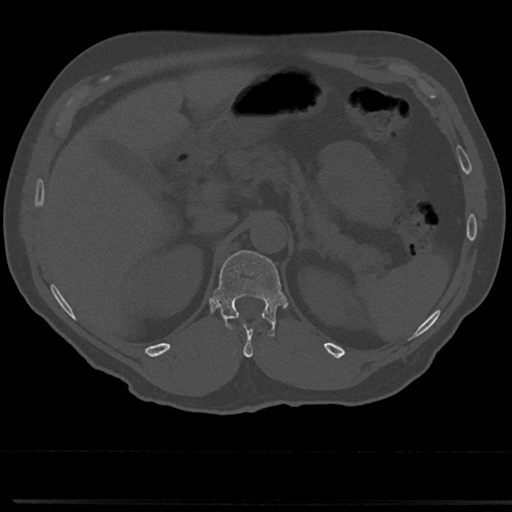
CT including the spine, one axial slice; position 163 of 817 along the scan axis; reconstruction kernel Br40s/3; 120 kVp; bone window (W 1800 / L 400 HU); 512 × 512 image matrix. Patient: male, 61 years. From the clinical record (not read from this slice): primary cancer: prostate.
Structures marked on this image (semi-automatic segmentation, software-assisted and operator-edited):
- T11 vertebra: bounding box [x1, y1, x2, y2] px = [231, 324, 273, 356]
- T12 vertebra: [215, 249, 284, 335]